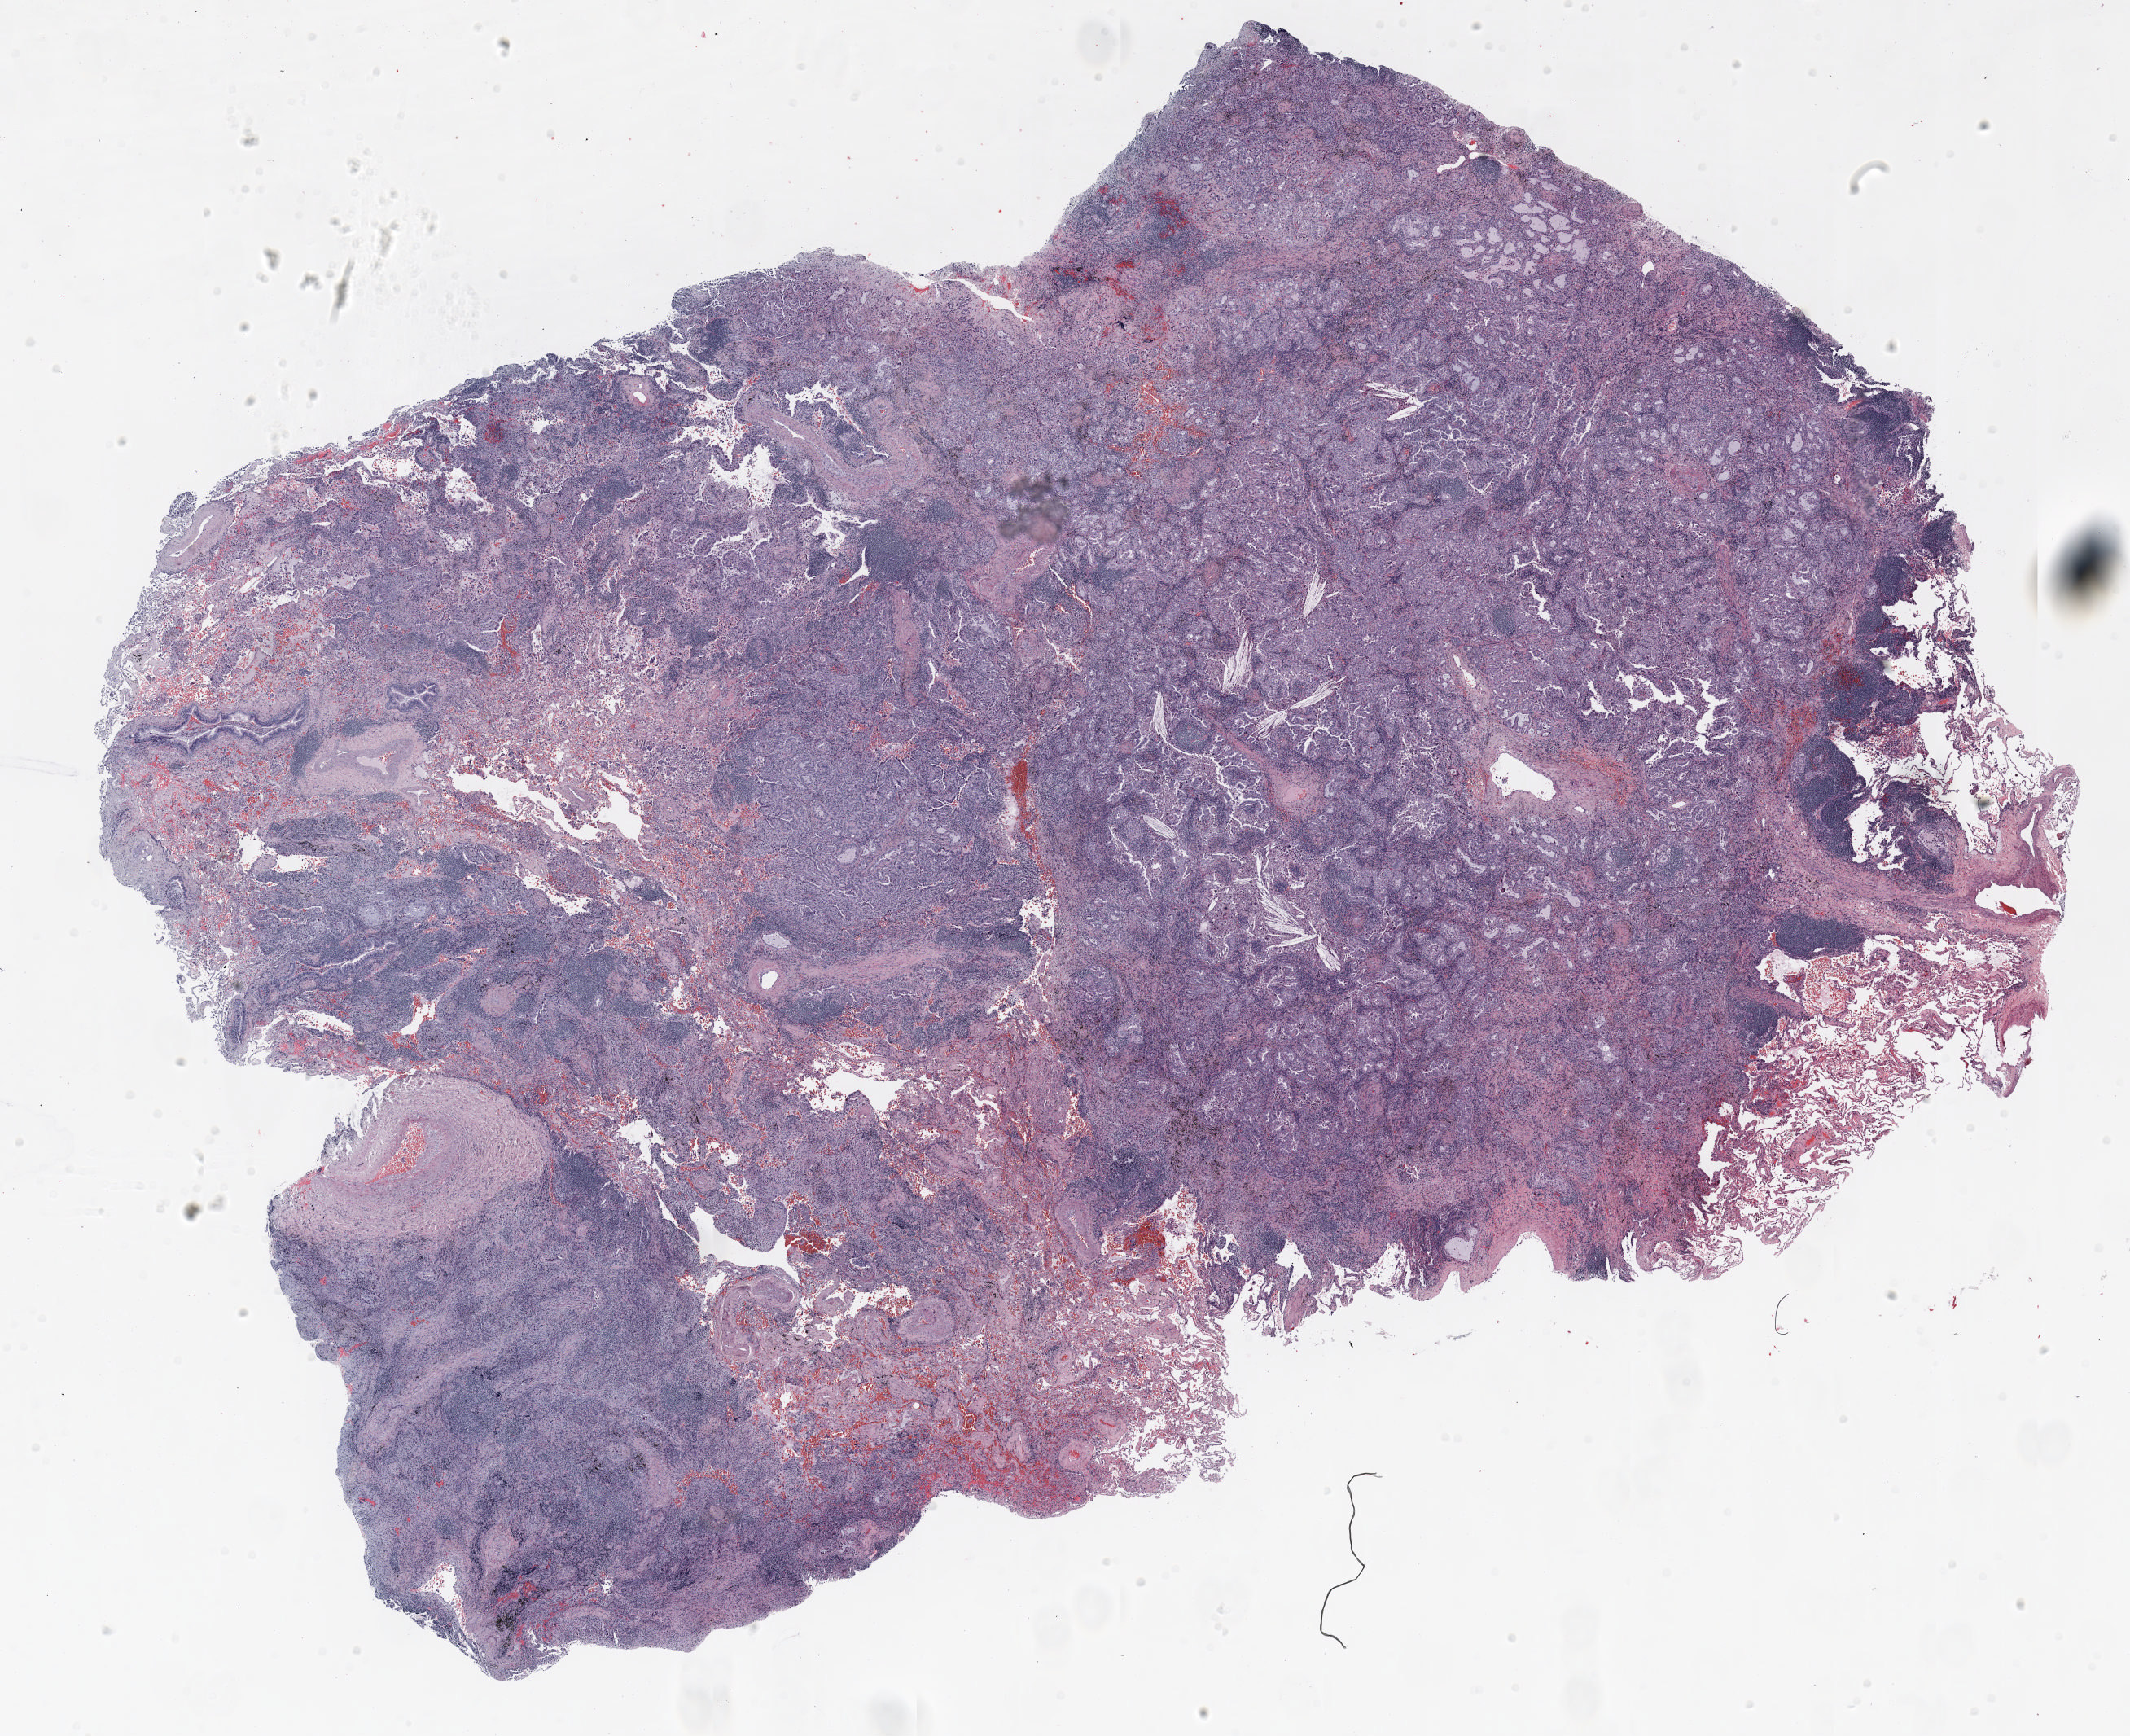
Whole-slide histology image, Hematoxylin and eosin (H&E) stained, low-resolution overview of the scanned area, about 21.0 x 17.1 mm. Formalin-fixed paraffin-embedded (FFPE) section. Lung tissue. Male, age 64 at enrolment. Current smoker at enrolment. Grade: well differentiated (G1).
Primary tumour location (clinical record): right upper lobe. Tumour size (pathology): 19 mm. ICD-O-3 topography: upper lobe of lung (C34.1). Participant's lung-cancer diagnosis: Adenocarcinoma, NOS. Stage (AJCC 6th edition): IA.